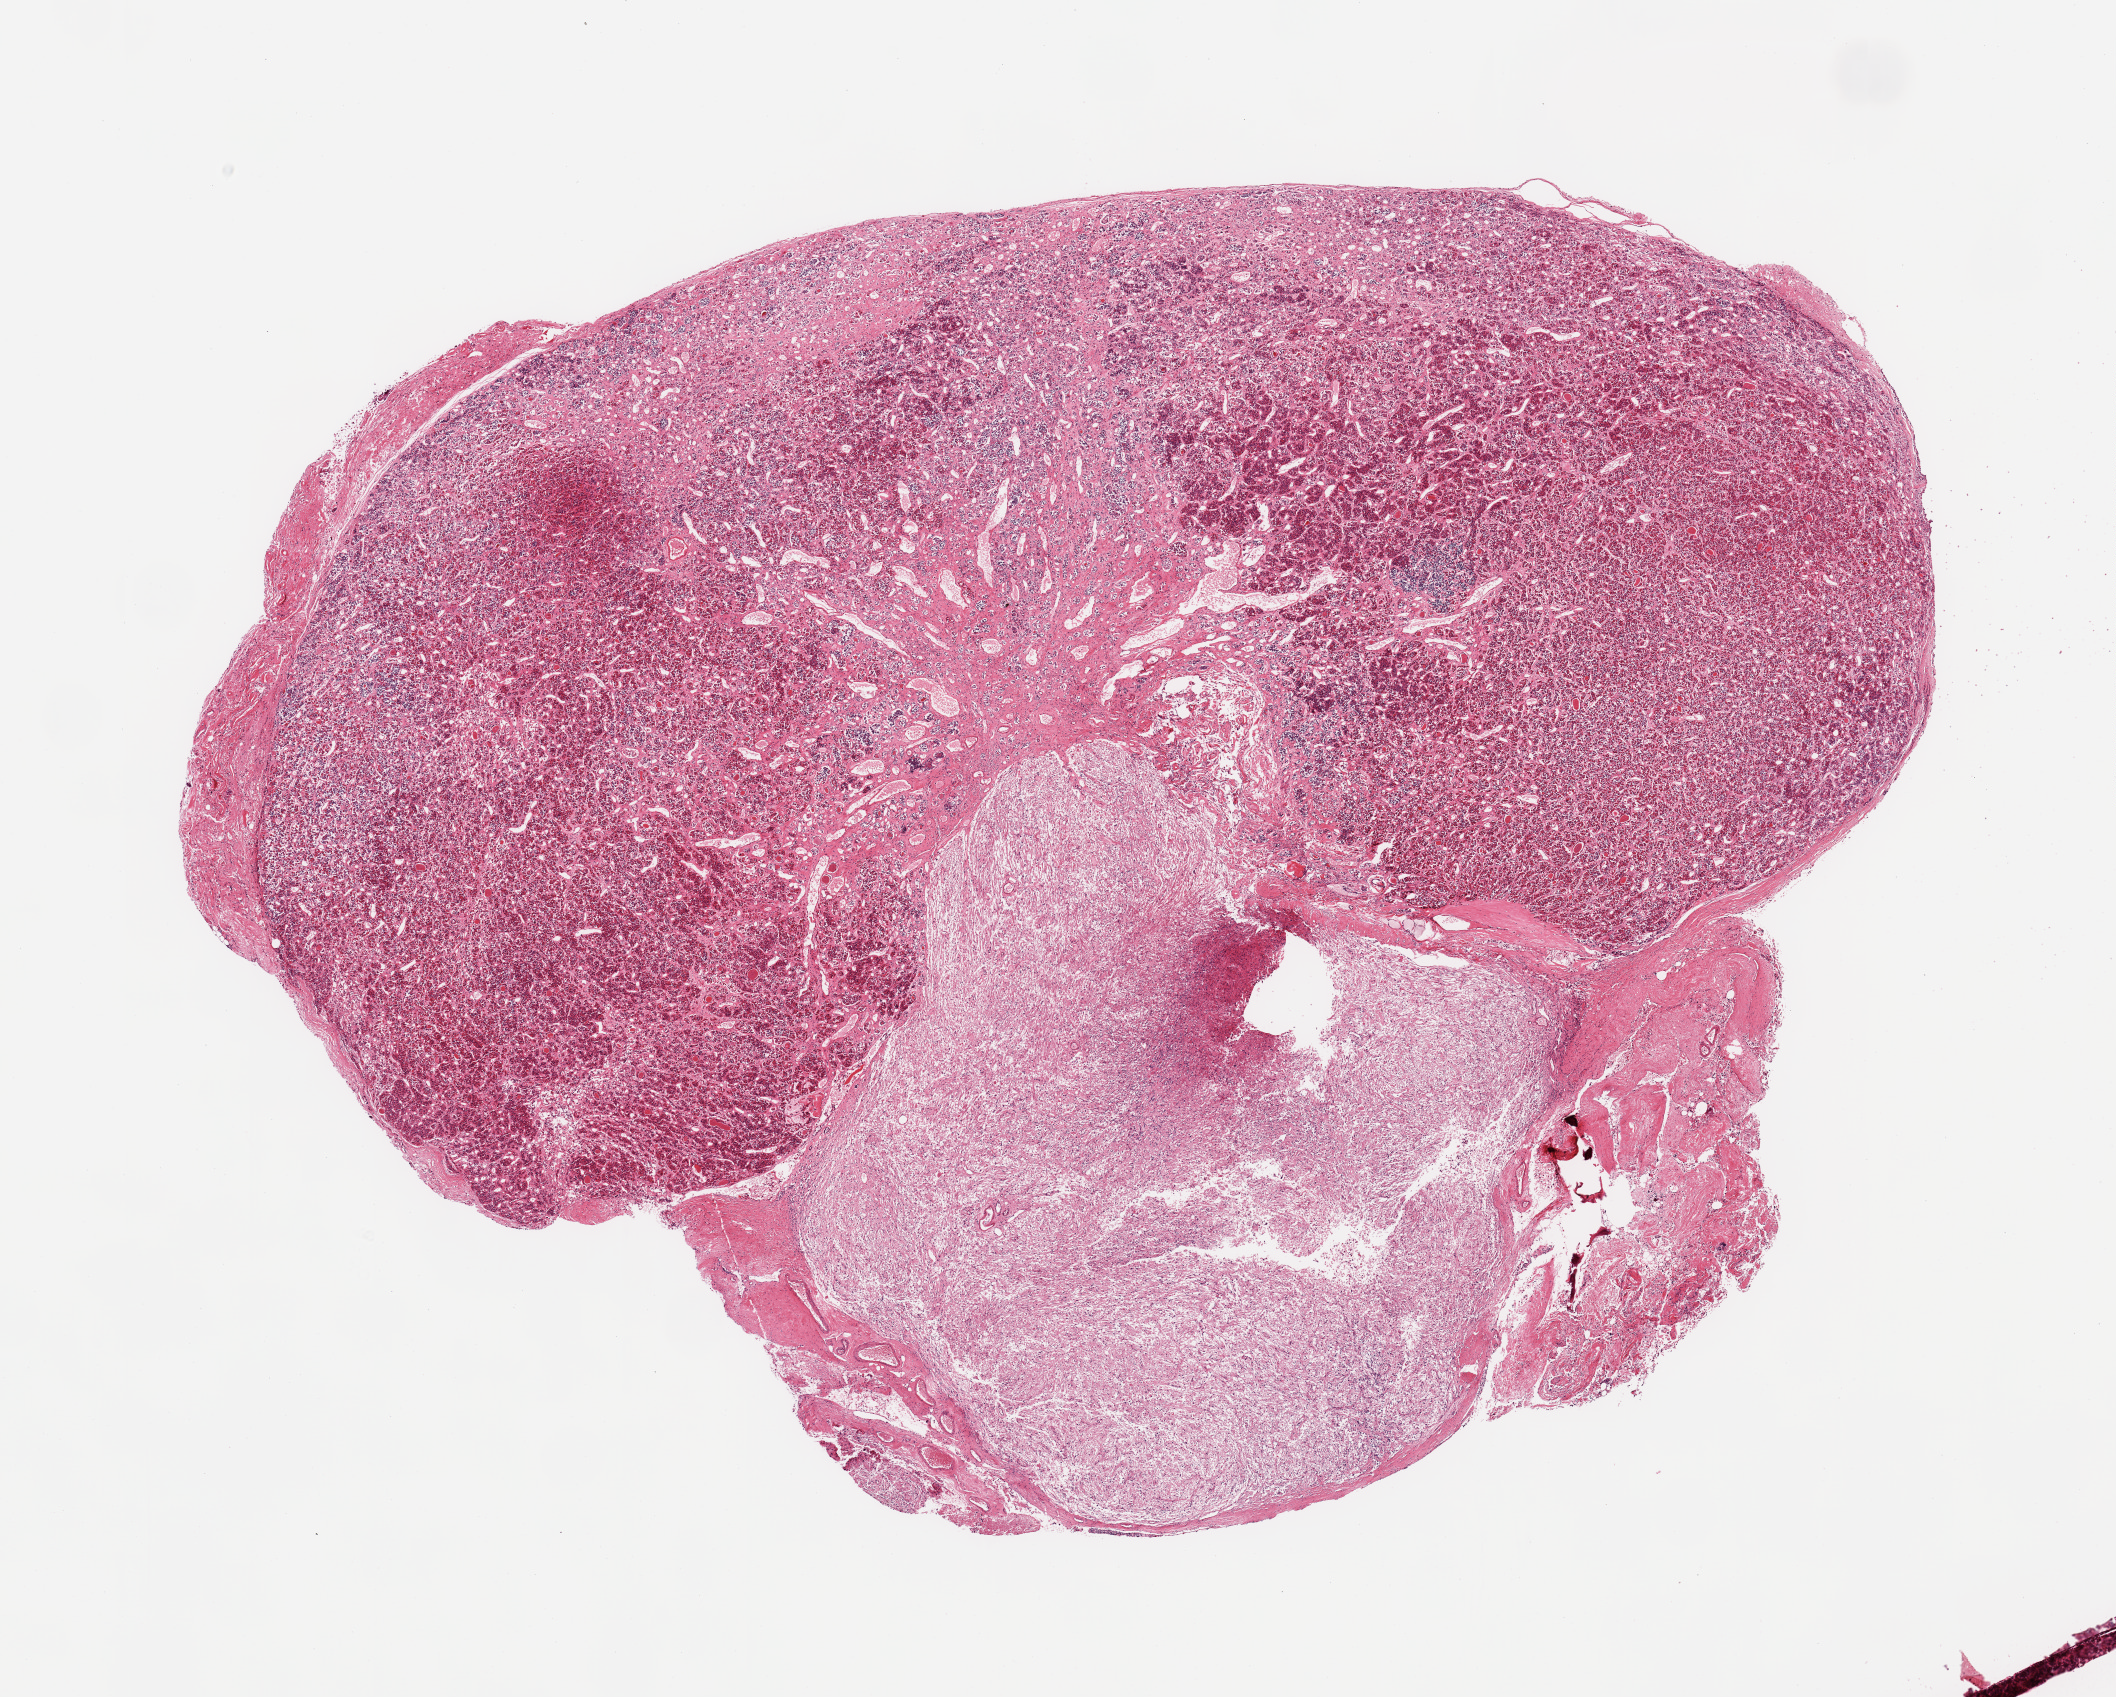
H&E whole-slide image, brightfield, low-resolution overview of the scanned area, about 16.7 x 13.4 mm (from a 20x scan); PAXgene-fixed paraffin-embedded (PFPE) section; section of pituitary (target tissue); donor tissue sample. Donor sex: female.
Pathologist's review note for this sample: 1 piece; well dissected neuro- and adenohypophysis.